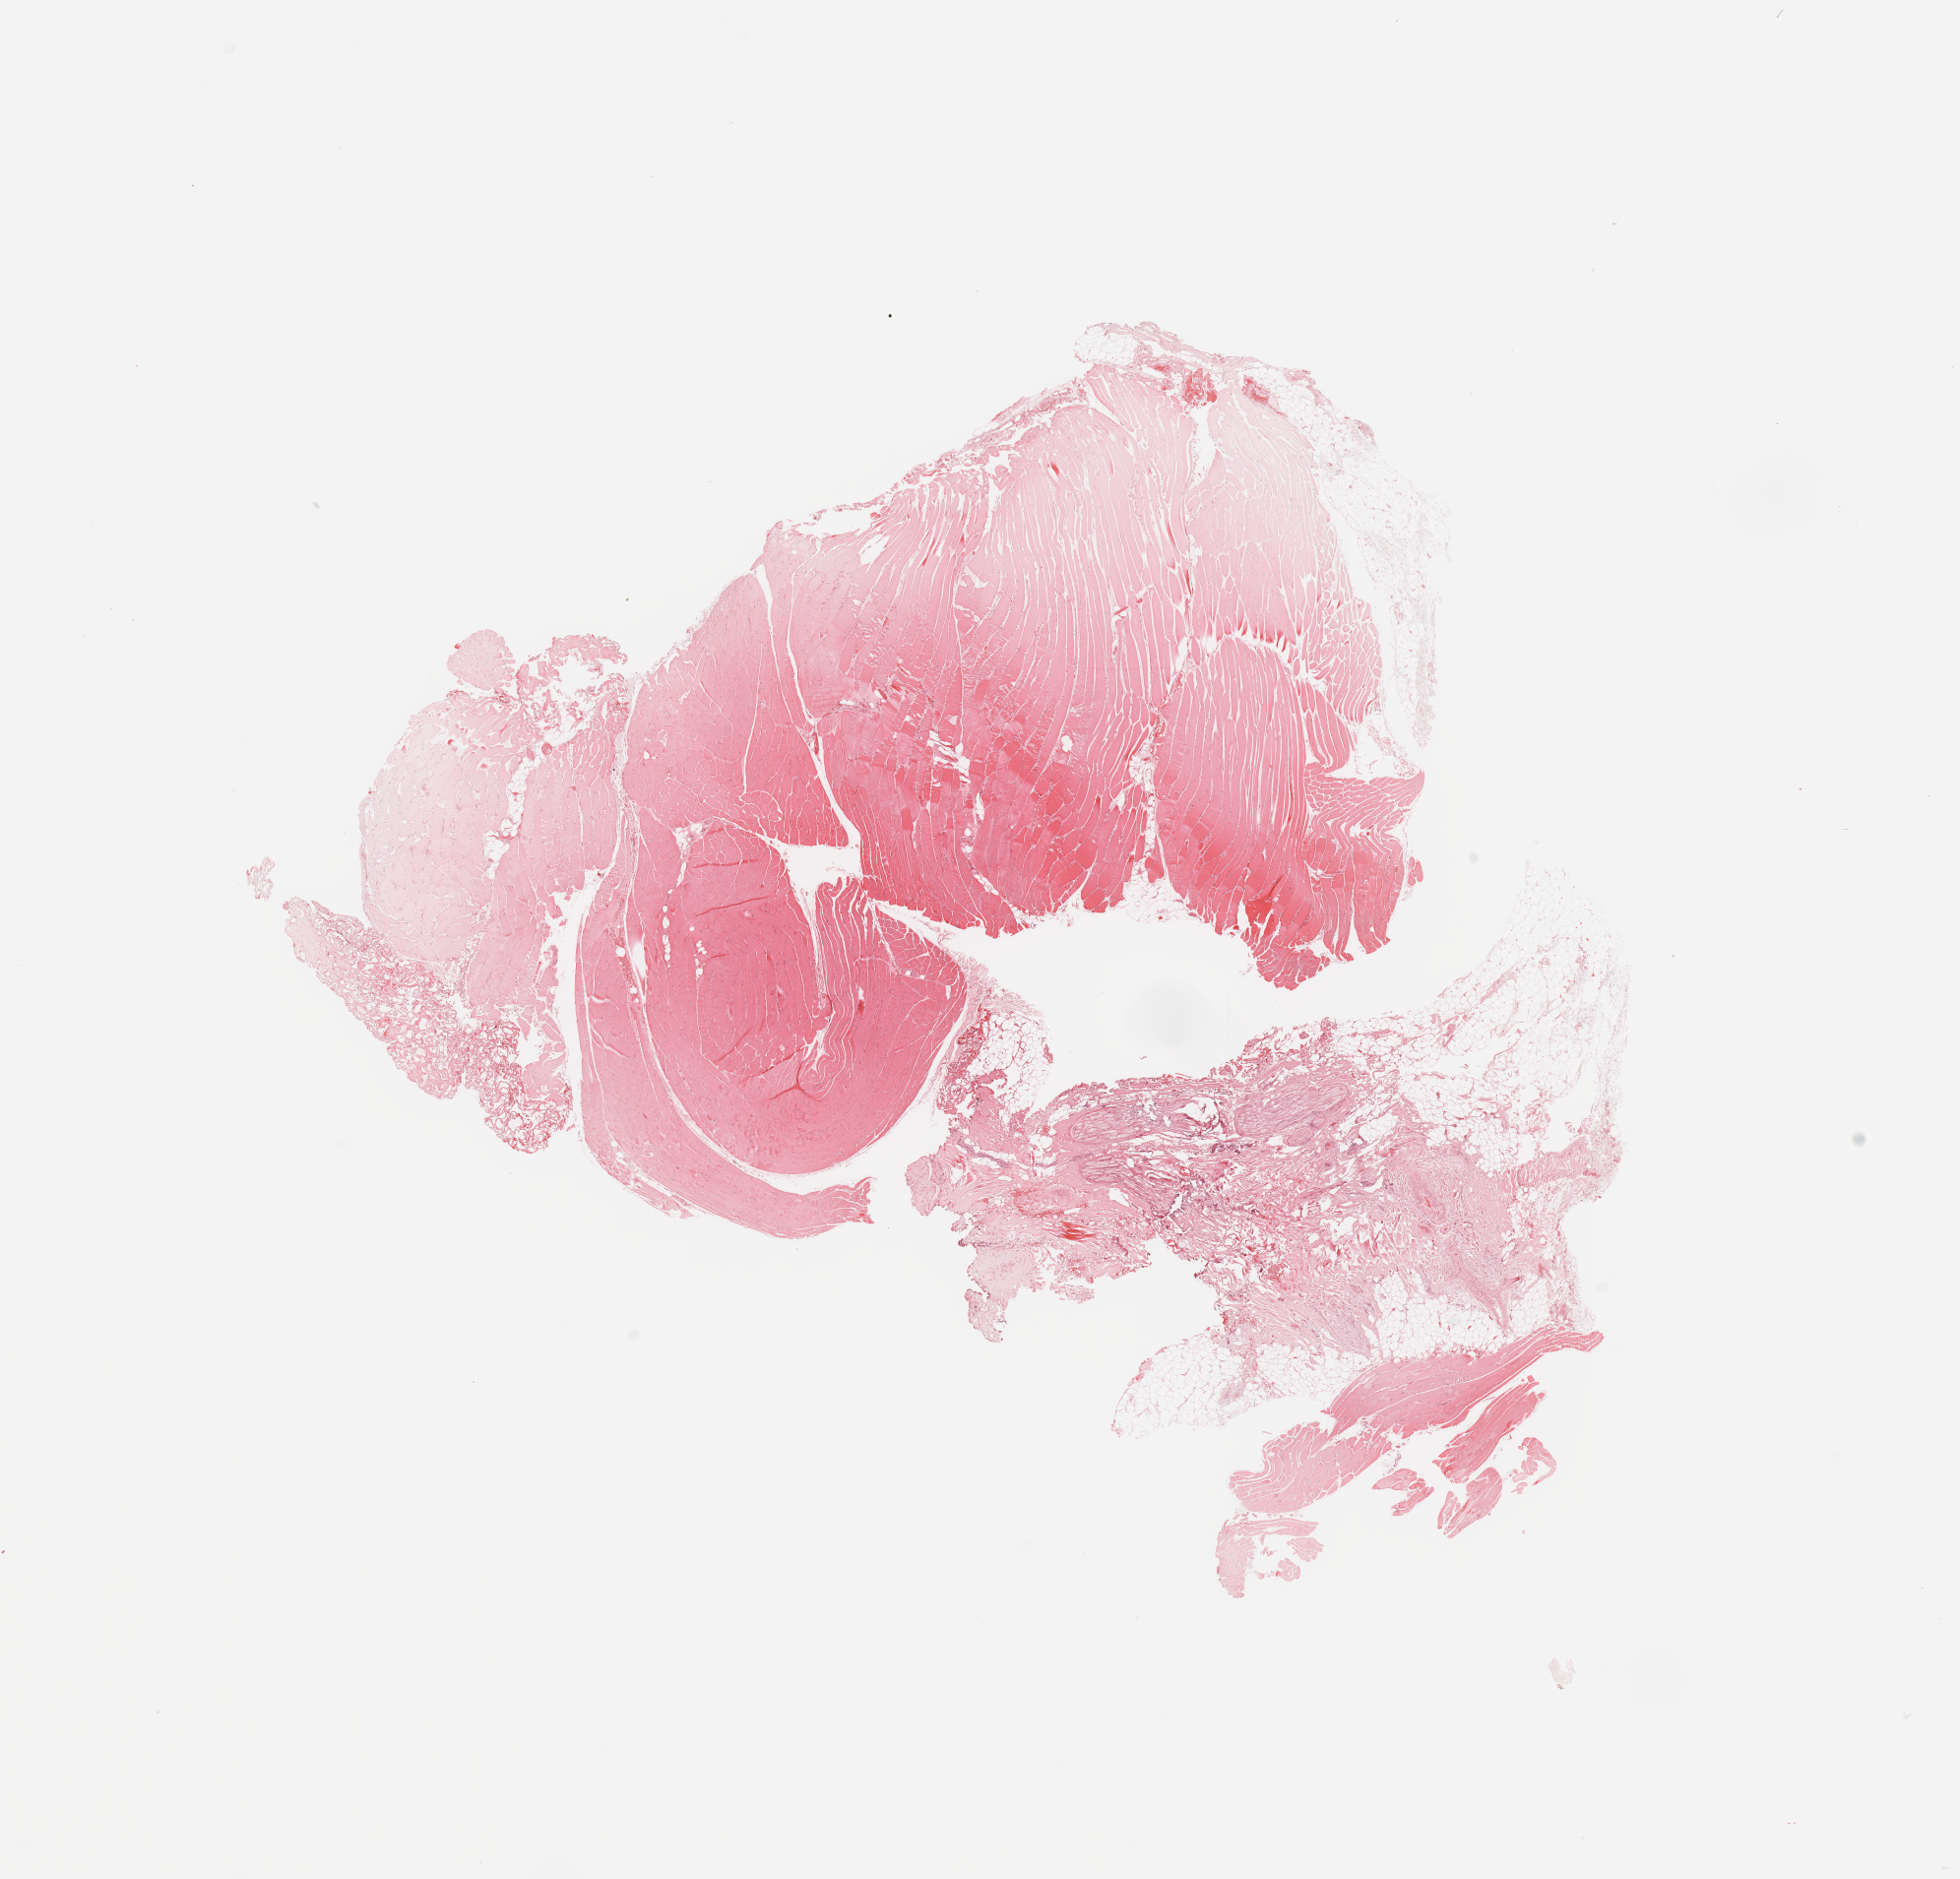
Whole-slide histology image, H&E-stained, low-resolution overview of the scanned area, about 15.8 x 15.1 mm (acquisition: 20x scan). Normal (non-tumour) tissue sample. Female, 23 y/o.
- this section: normal (non-tumour) tissue from the same patient
- patient diagnosis (cohort enrolment): sarcoma (site not recorded at cohort level)